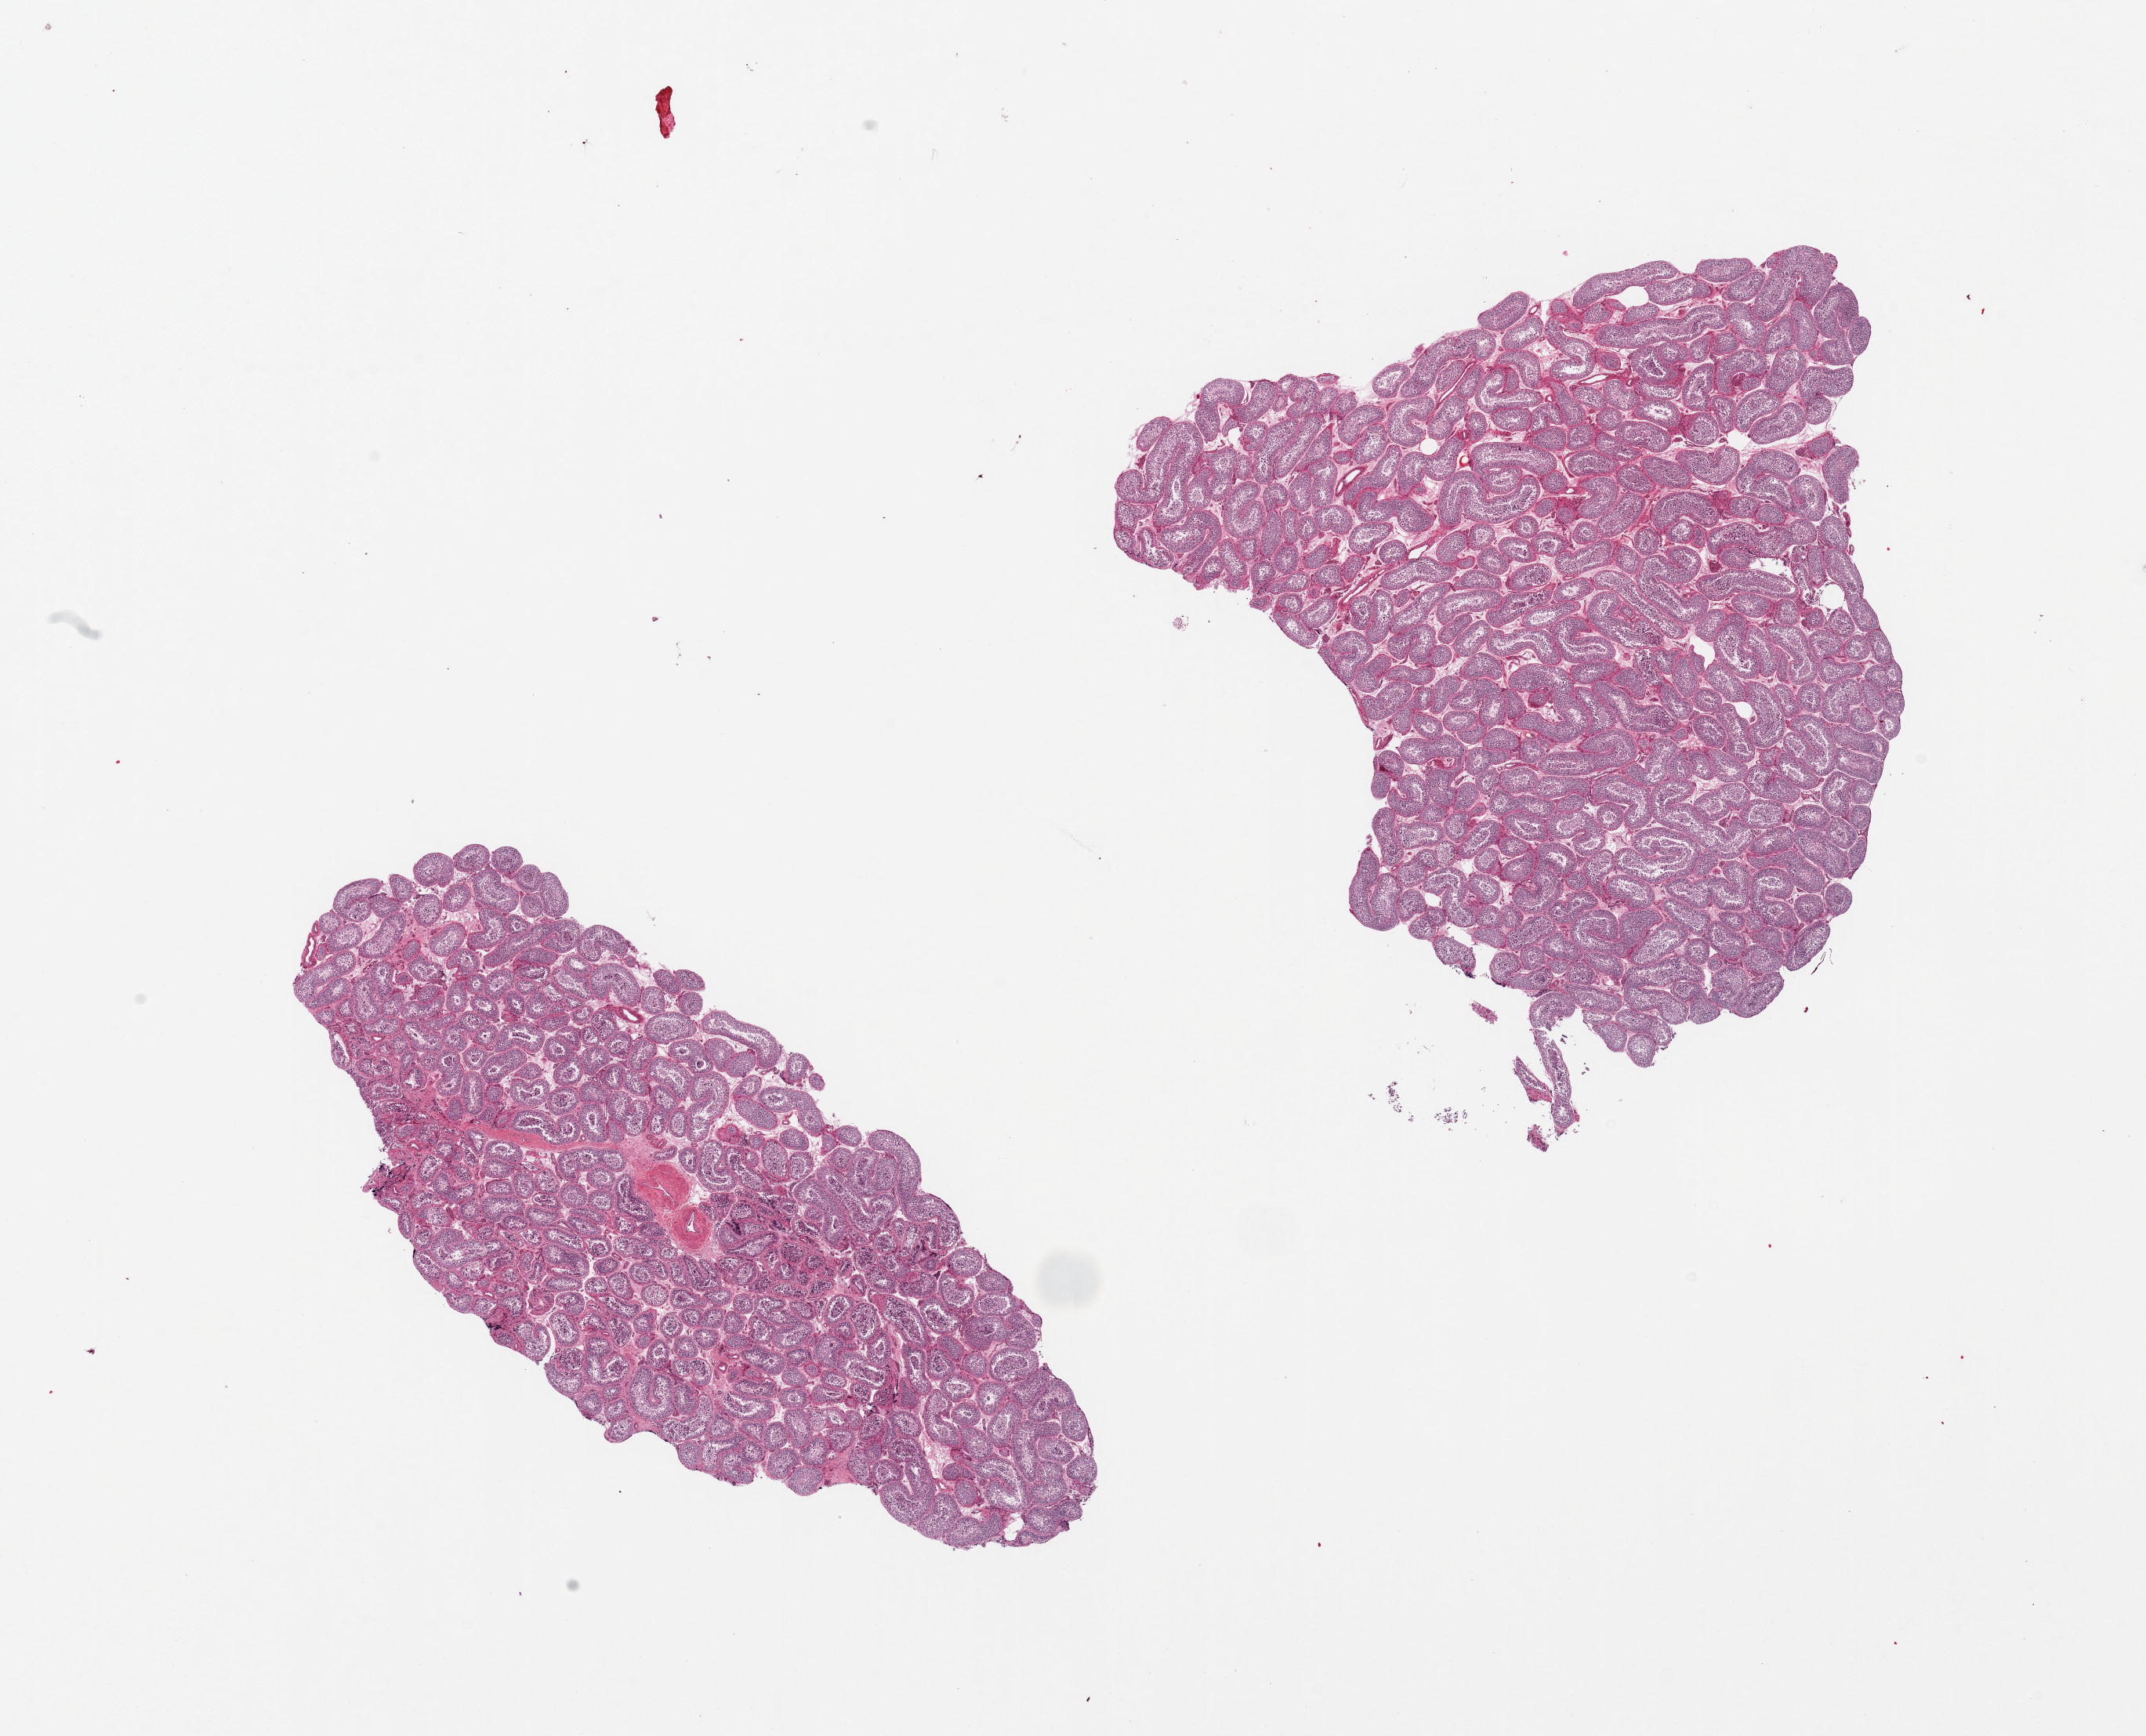
Whole-slide image, hematoxylin and eosin (H&E) stain, brightfield, shown as a low-resolution overview of the whole scanned area (about 21.7 x 17.5 mm). PAXgene-fixed paraffin-embedded (PFPE) section. Sampled site (target tissue): testis. Tissue donor sample. Male donor.
Reviewer comment on this tissue sample: 2 pieces. spermatogenesis.